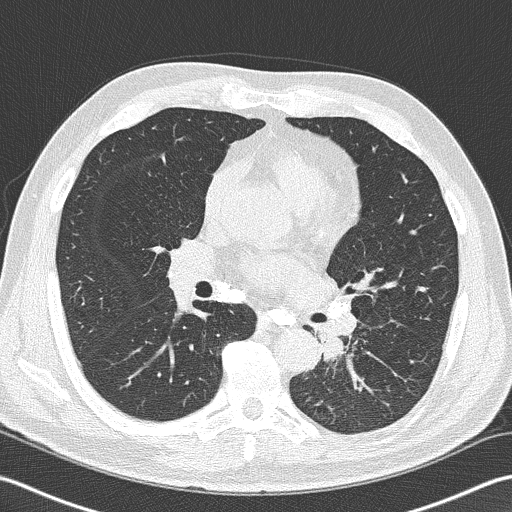
Axial slice from a low-dose chest CT screening exam, second annual screen, lung window (W 1500 / L -600 HU), 2 mm slice thickness, 120 kVp, slice 78 of 170 in the series, 512 × 512 image matrix. Male participant, aged 57 years at enrolment. Former smoker at enrolment.
Lesion marked by an expert reader, box from (x=293, y=299) to (x=373, y=380) px. Screening reader's record for this exam (one nodule recorded; not confirmed to be the boxed lesion): non-calcified nodule or mass ≥4 mm, left lower lobe, 40 × 30 mm, spiculated (stellate) margins, soft tissue attenuation, pre-existing on the prior screen: no. Participant outcome: lung cancer diagnosed 9 days after this screen — squamous cell carcinoma, NOS, left lower lobe, moderately differentiated (G2), stage IIIB (AJCC 6th edition), 38 mm at pathology.